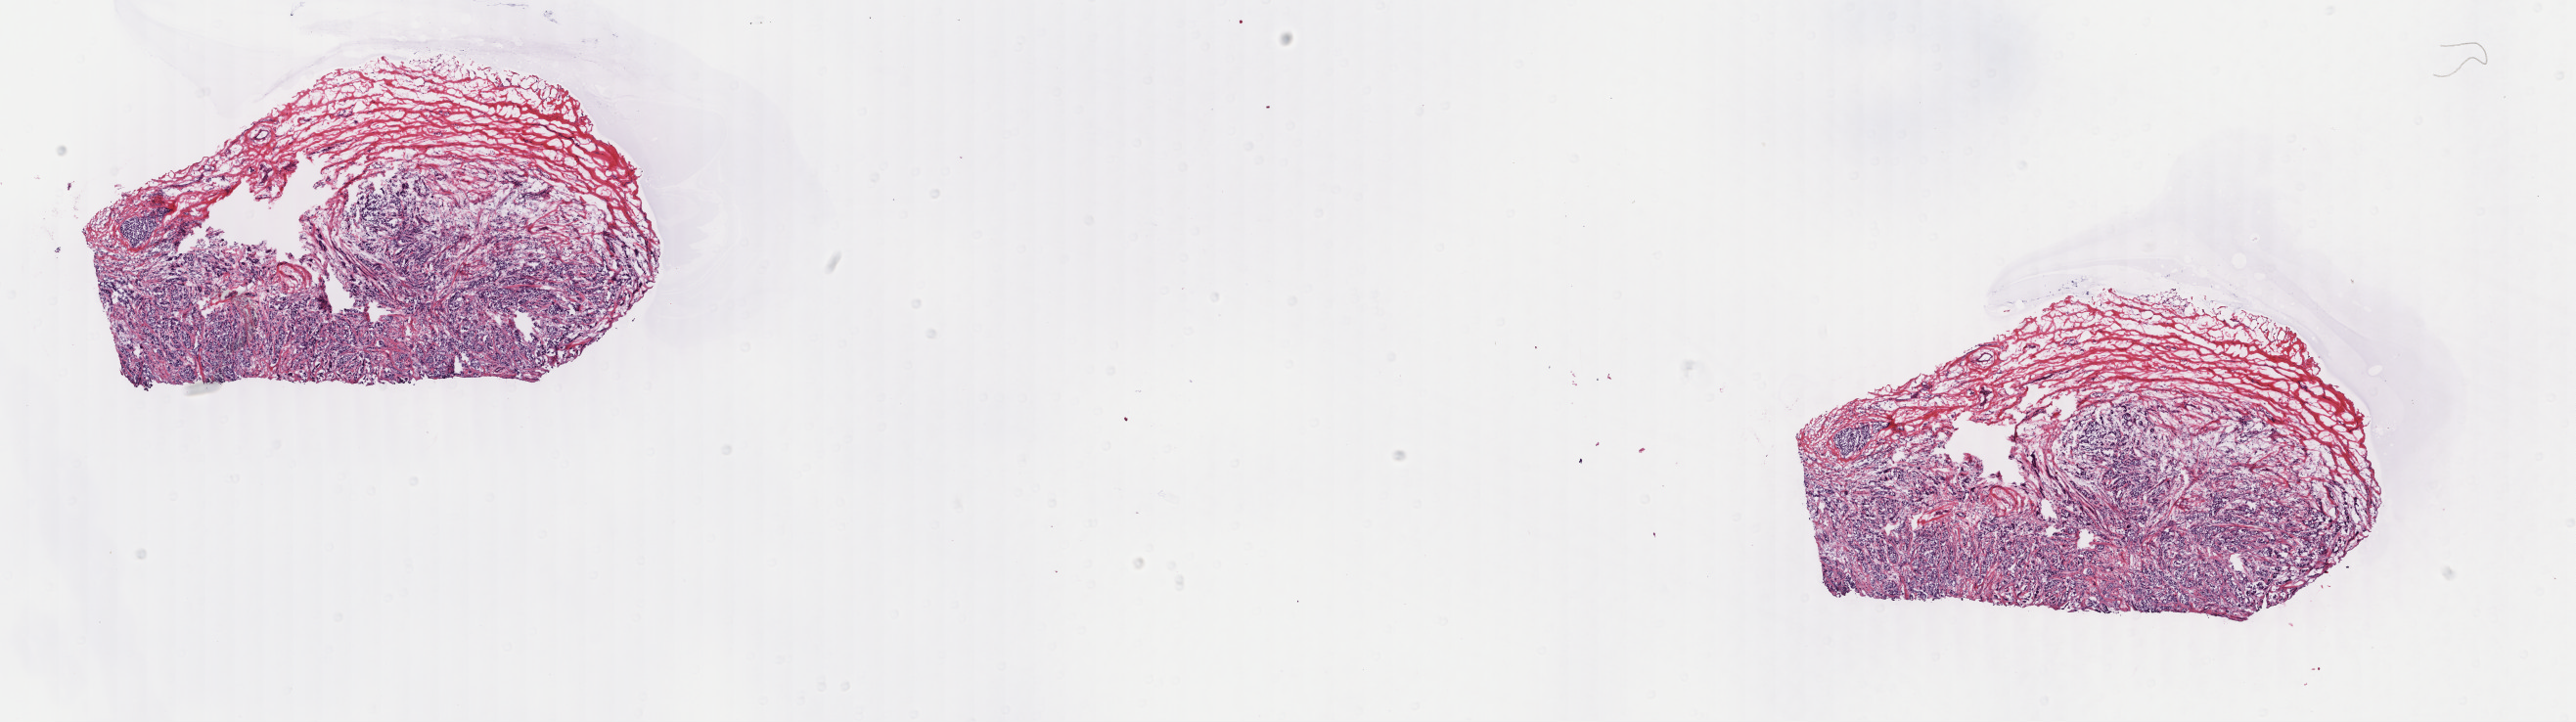
Digitized H&E tissue section (whole slide), a low-resolution overview of the entire scanned area, about 20.9 x 5.9 mm (slide scanned at 40x), frozen section, breast, primary tumour sample. Female, age 62 years at initial diagnosis. Slide review estimates, as recorded: tumour cells 80%, tumour nuclei 85%, normal cells 0%, stromal cells 20%, necrosis 0%. Inflammatory infiltration, as recorded: lymphocyte infiltration 2%, monocyte infiltration 0%, neutrophil infiltration 0%.
Lymph nodes positive (case pathology): 1 of 23 examined. Diagnosis: Infiltrating duct carcinoma, NOS. AJCC pathologic stage: IIB (6th edition).